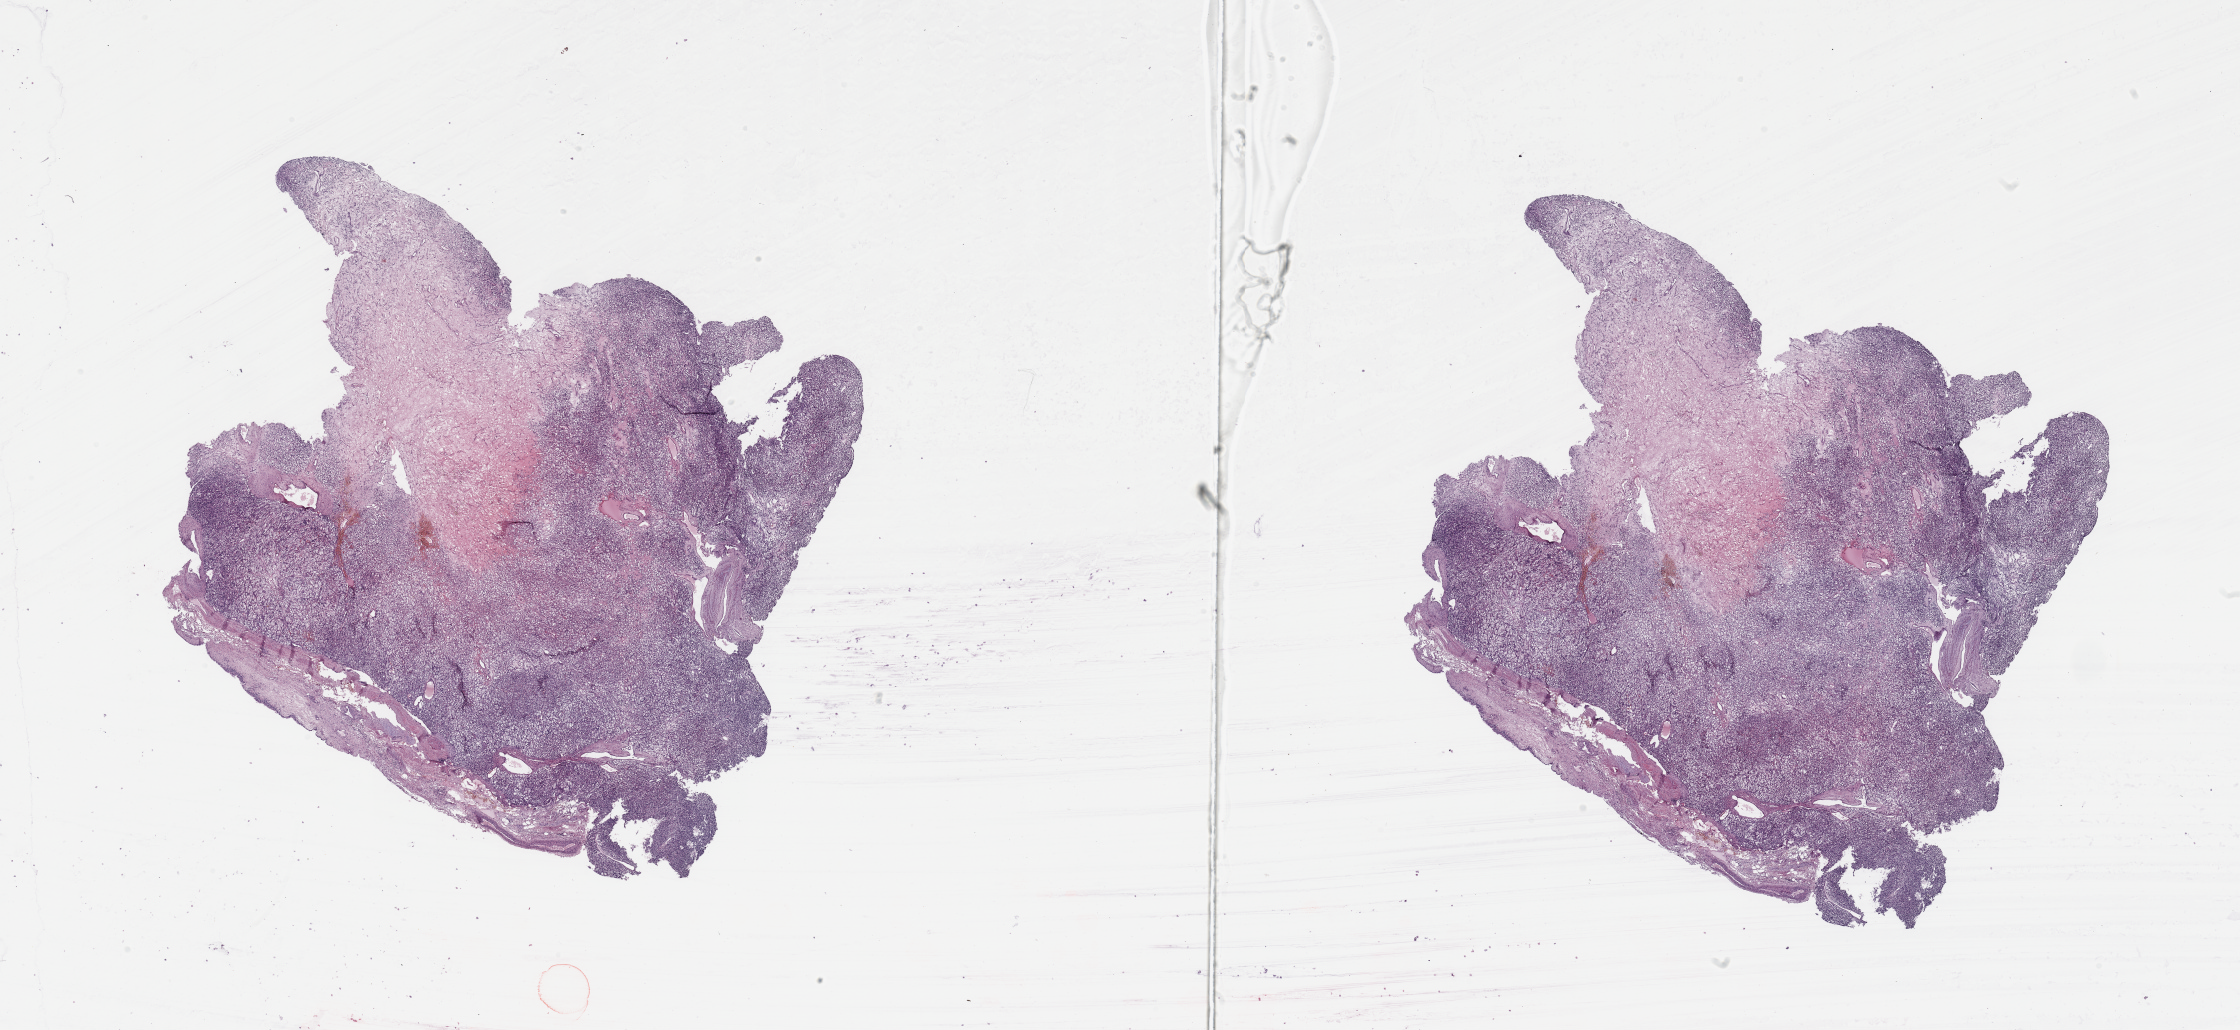
H&E-stained whole-slide image, whole scanned area (about 35.4 x 16.3 mm) shown as a low-resolution overview. Tumour tissue sample, kidney. Female, 66 y/o. Histologic grade: G2 (moderately differentiated).
AJCC pathologic stage: III. Diagnosis: Renal cell carcinoma, NOS. Primary tumour site (as recorded): upper pole.